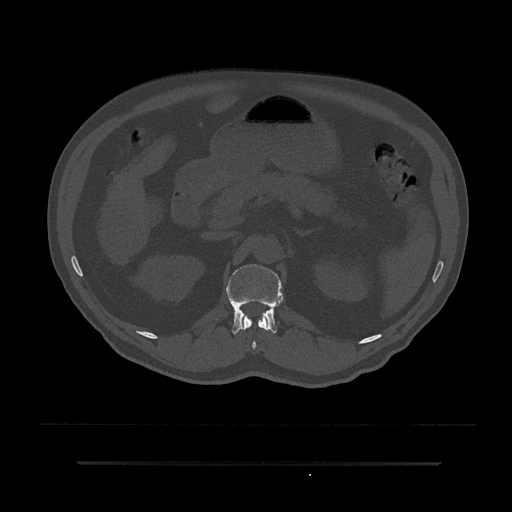
CT including the spine, one axial slice. Slice 170 of 797 in the series (ordered by position). Bone window (W 1800 / L 400 HU). 512 × 512 image matrix, field of view 464 × 464 mm. Patient: male, 59 years. Case-level facts recorded for this patient, not image findings: primary cancer: bile ducts; vertebrae with lytic lesions (as recorded): T10.
Annotated regions visible in this slice (semi-automatically segmented with operator editing):
- L1 vertebra: box from (x=226, y=264) to (x=283, y=334) px
- T12 vertebra: (x=241, y=315)–(x=268, y=350)